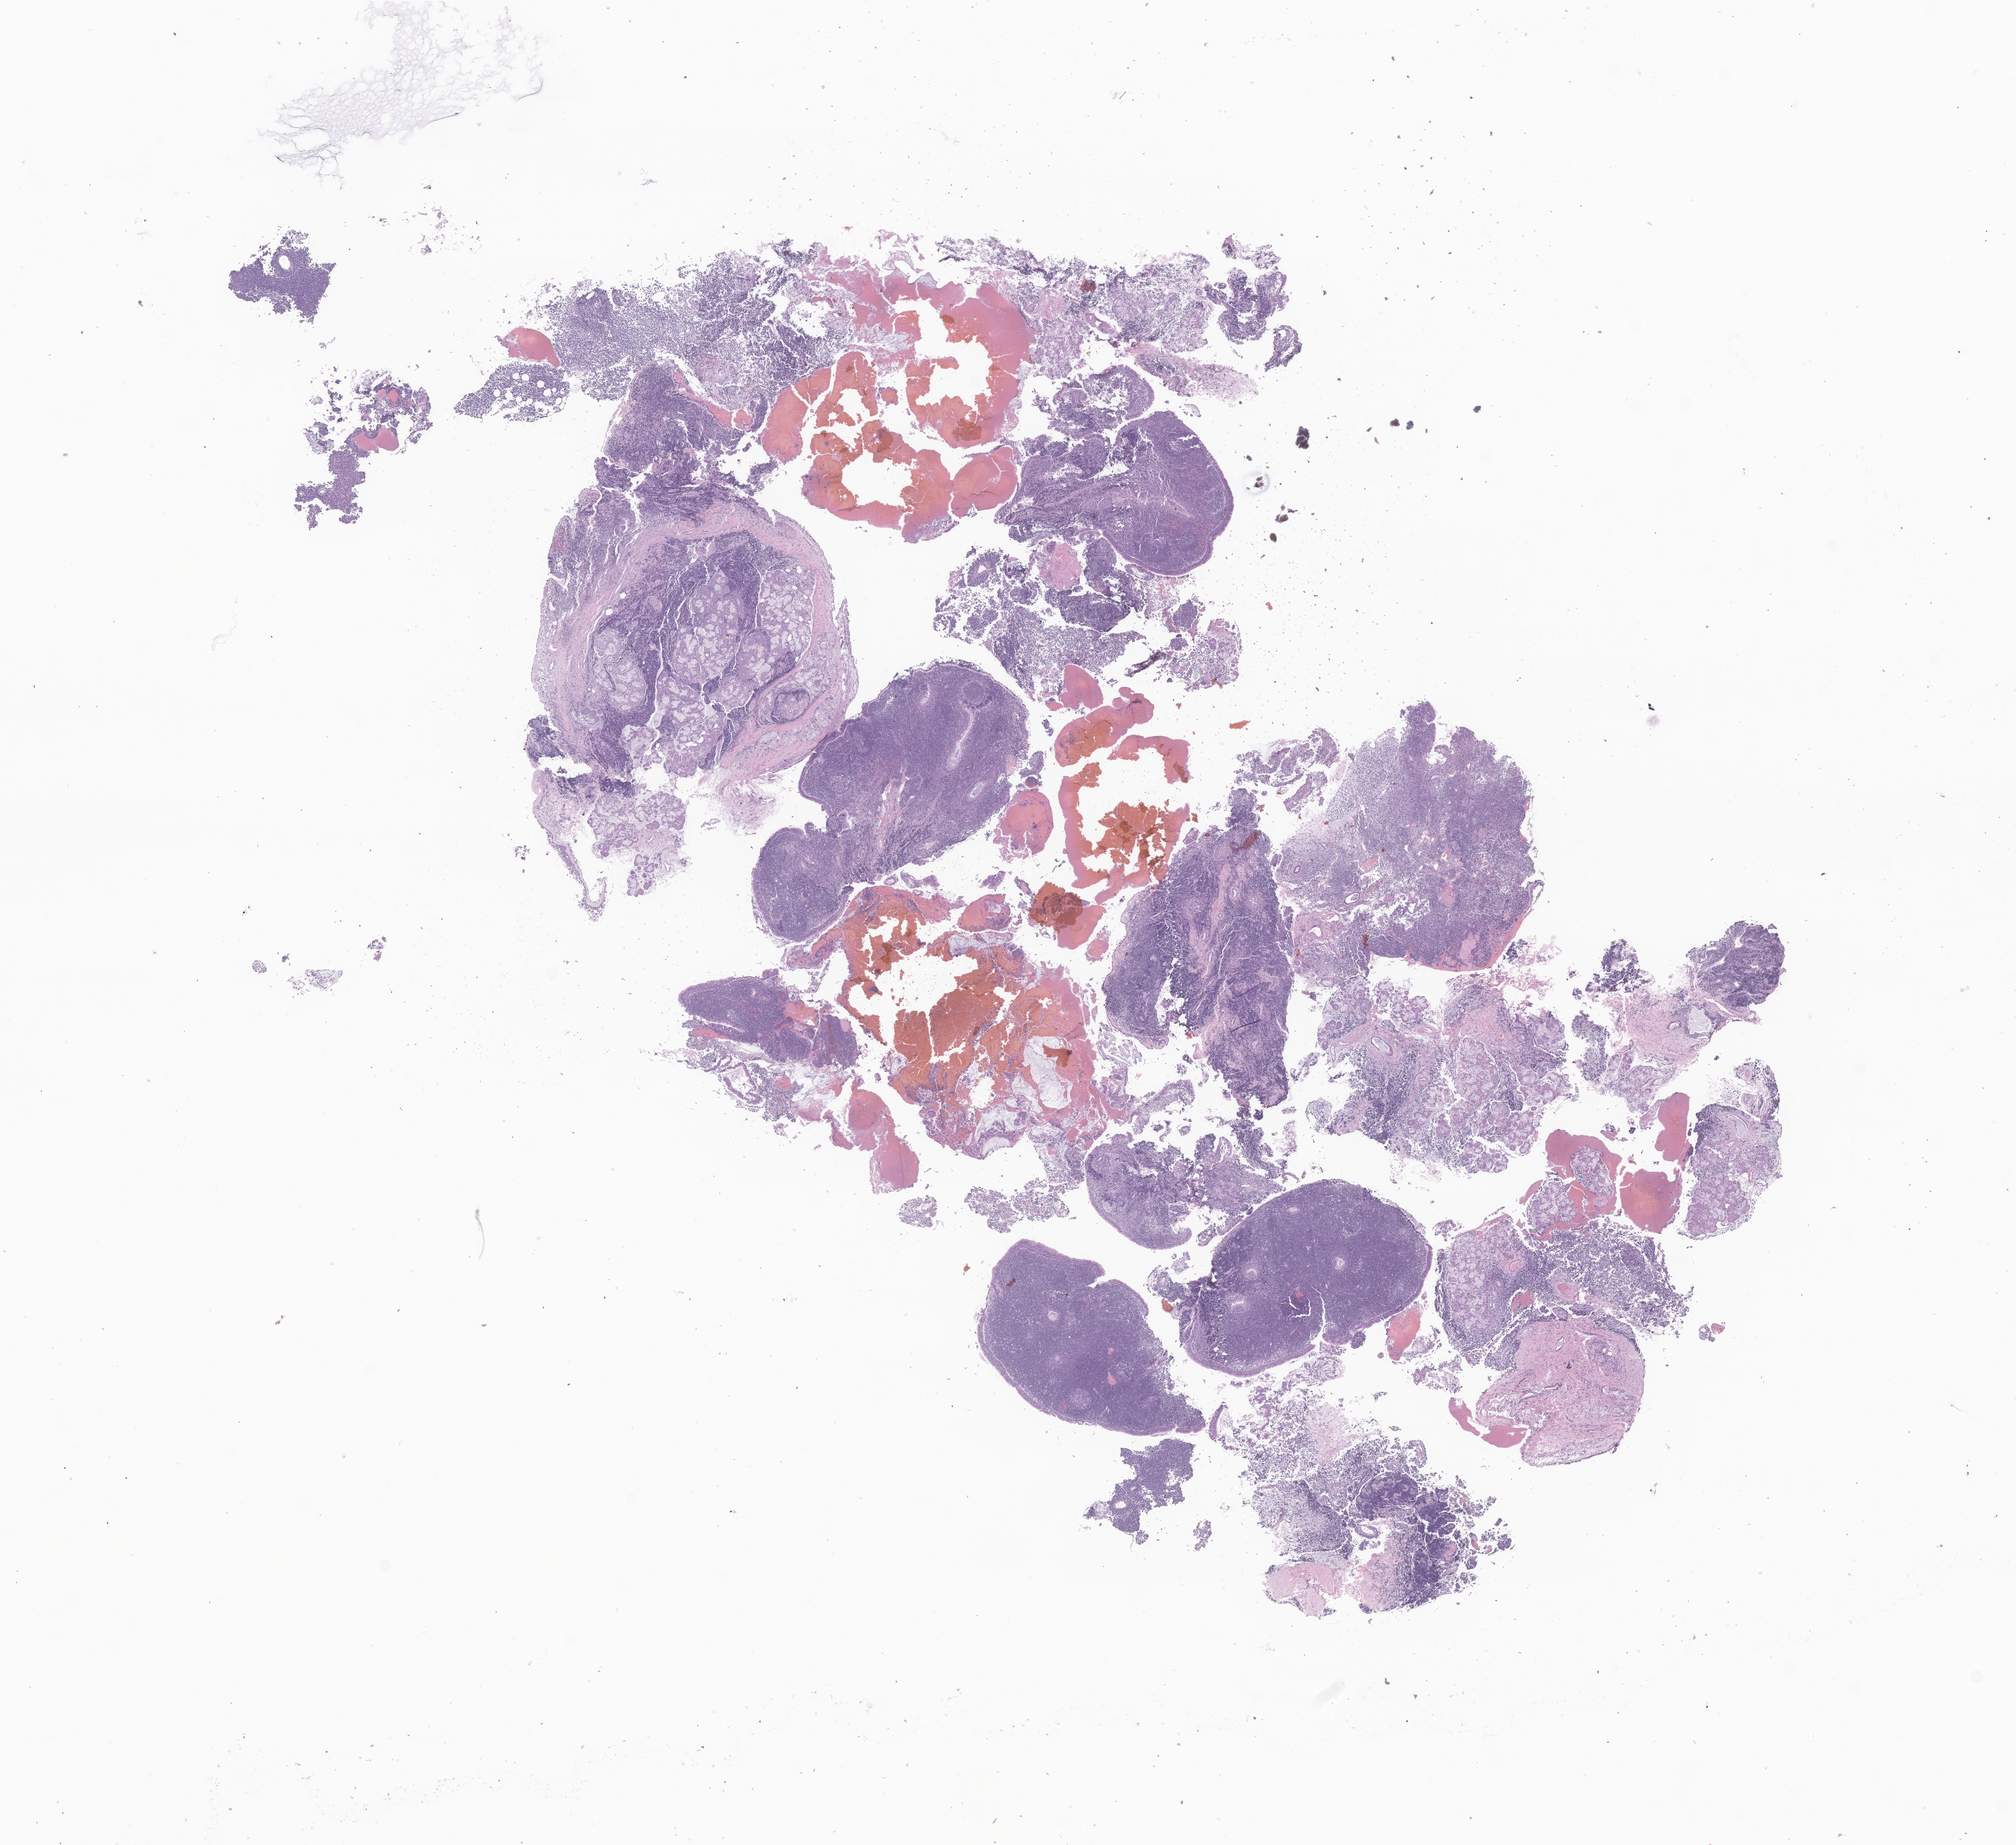
H&E whole-slide image of tumor tissue from the superior wall of nasopharynx — whole scanned area (about 16.3 x 14.9 mm) shown as a low-resolution overview. Formalin-fixed, paraffin-embedded (FFPE) tissue. Male patient, age 162 months (13 years 6 months).
Diagnosis (ICD-O-3 morphology term): Rhabdomyosarcoma, NOS.